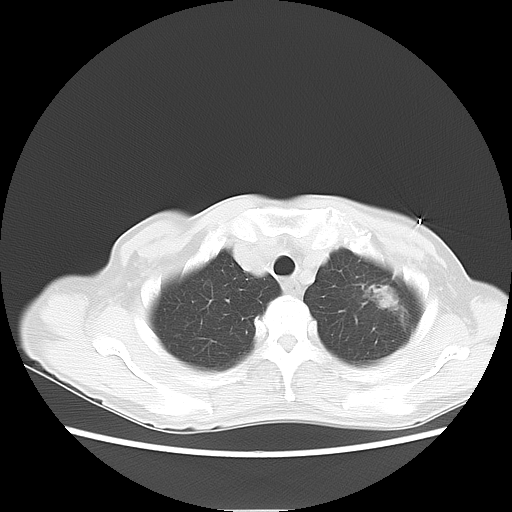
Chest CT, one axial slice. Position 12 of 14 along the scan axis. Reconstruction kernel LUNG. 120 kVp. Lung window (W 1500 / L -600 HU). 5 mm slice thickness. 512 × 512 image matrix, field of view 350 × 350 mm. Female patient, age 71 years. From the clinical record (not read from this slice): clinical TNM (as recorded): T2 N0 M0.
Outlined on this slice (bounding box drawn by a radiologist):
- lung tumour (recorded histology: adenocarcinoma): bounding box <363,277,401,317> (left, top, right, bottom; pixels)